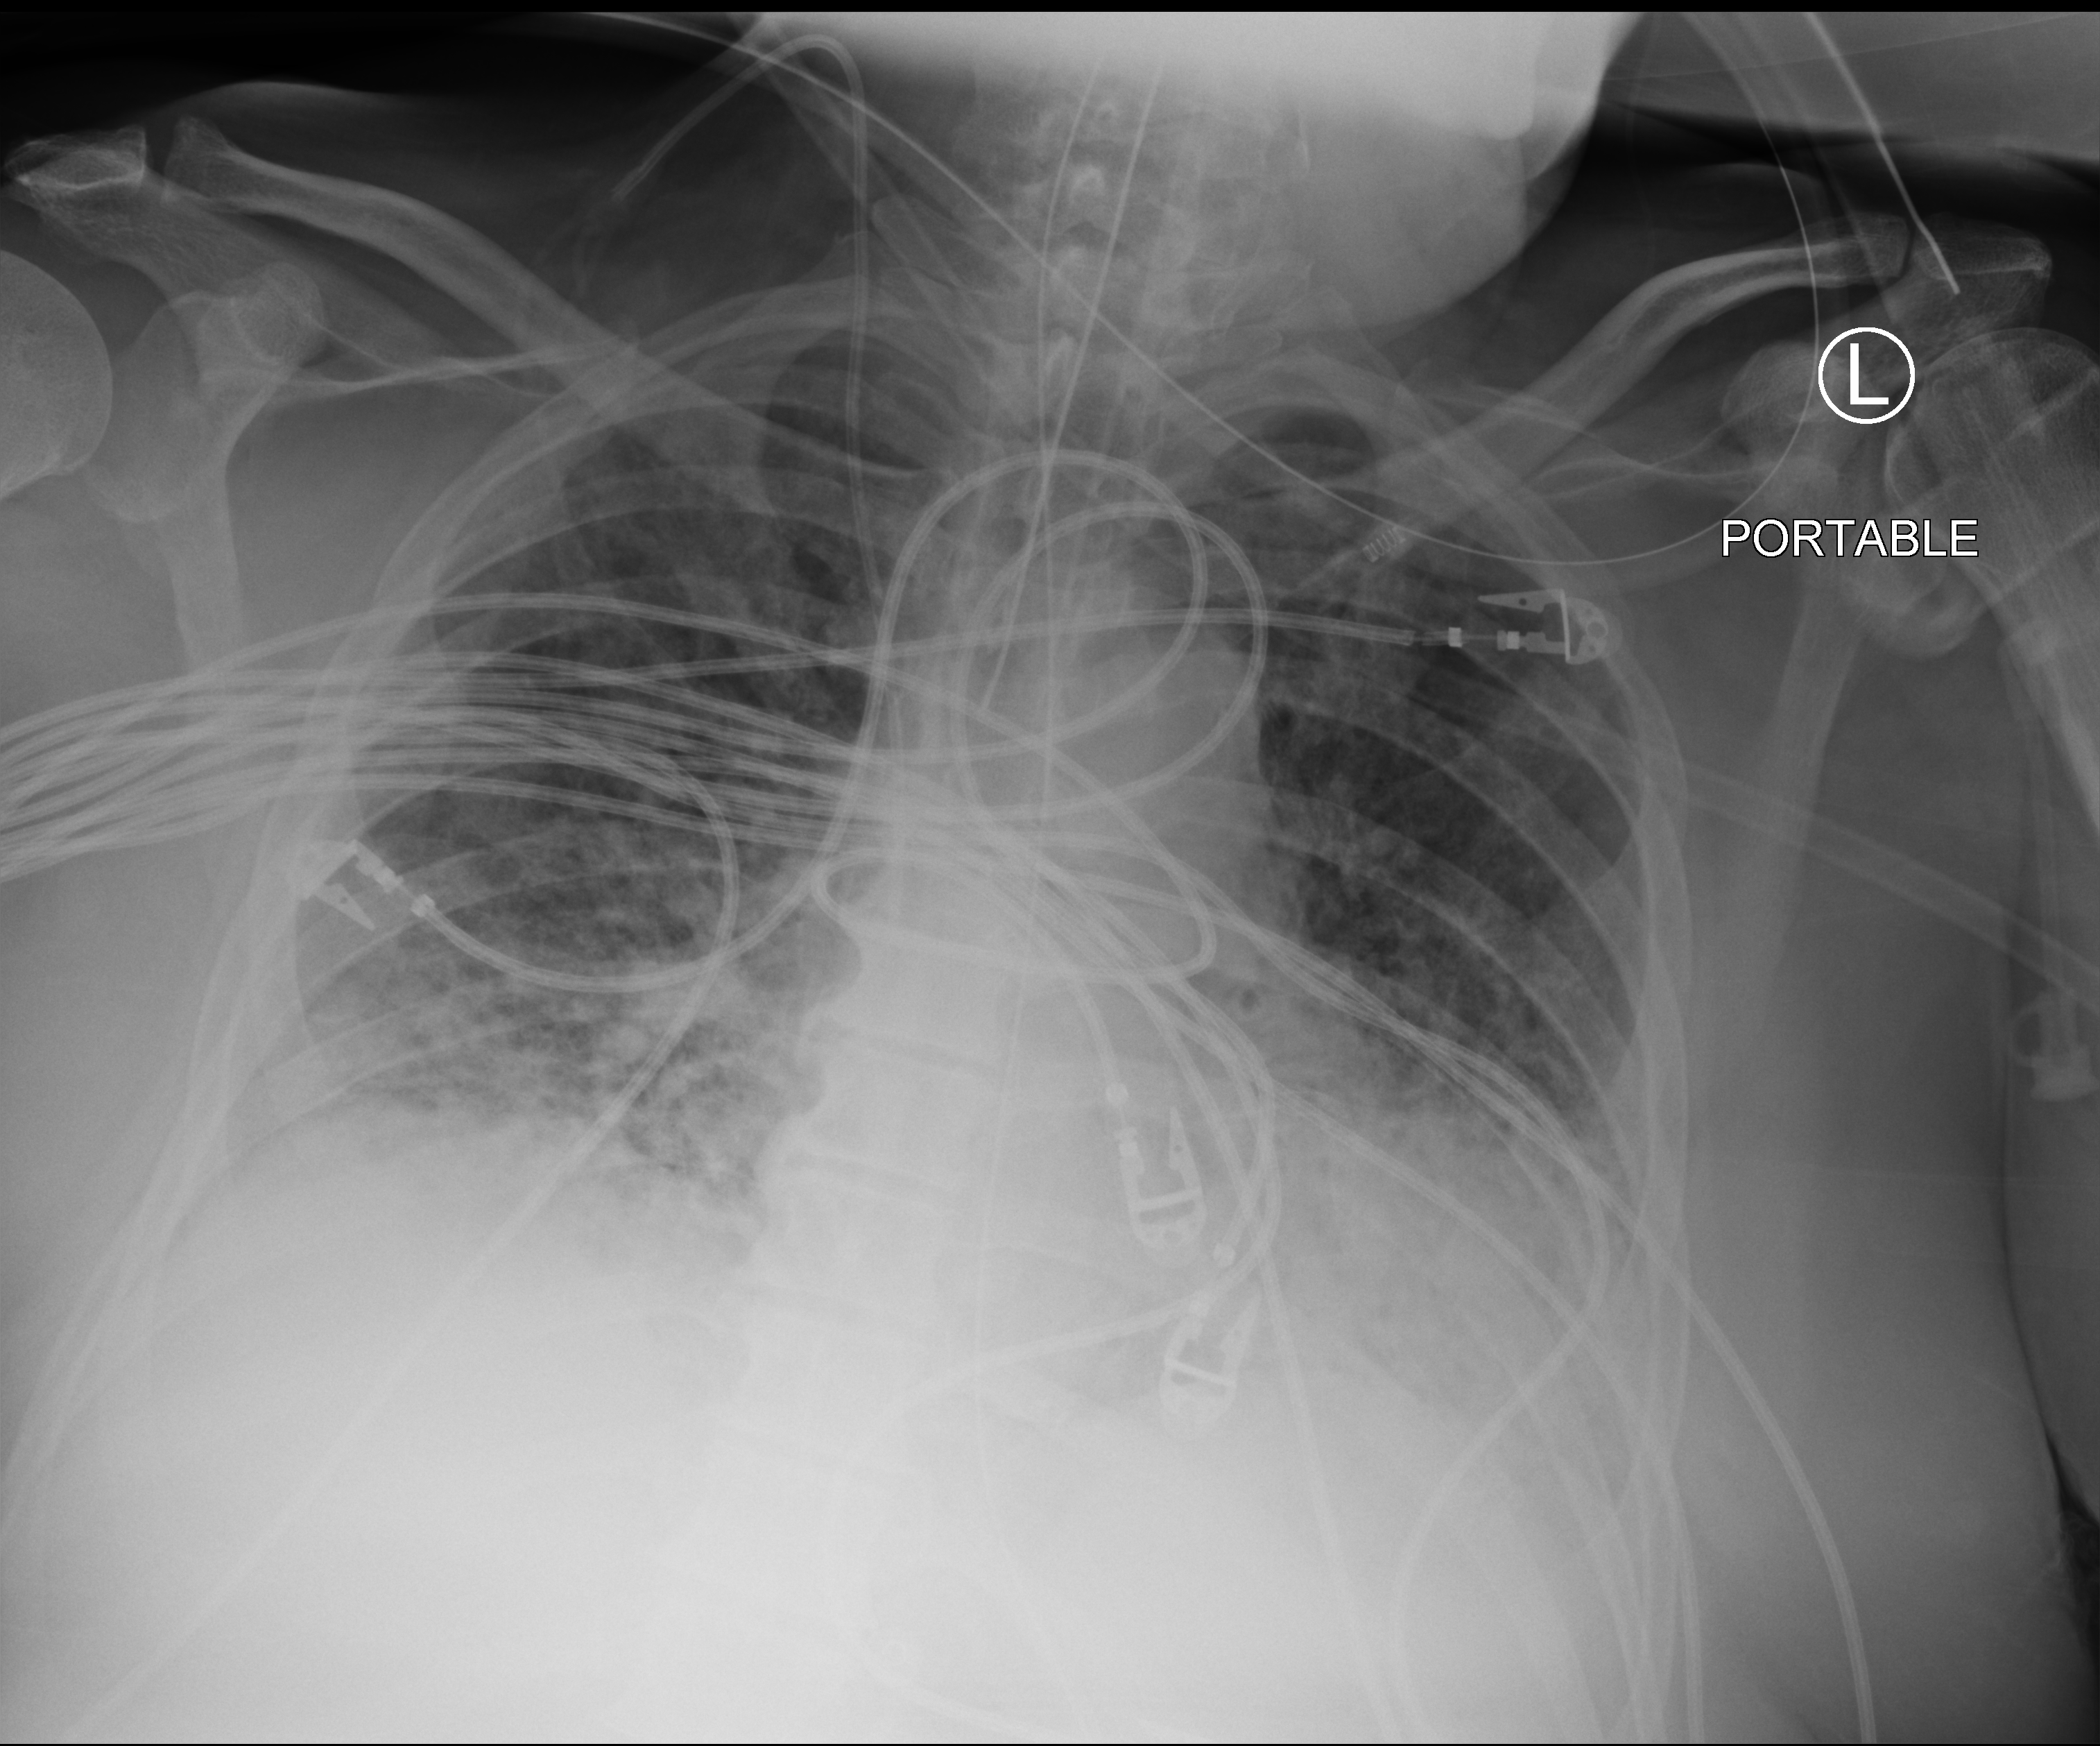
Chest X-ray (portable); anteroposterior (AP) projection. Male patient hospitalised with COVID-19, age 60–74 years.
Admission-level facts for this patient (not findings on this image; timing relative to this image not recorded):
- mechanically ventilated during this hospital stay: yes
- smoking status (admission record): former